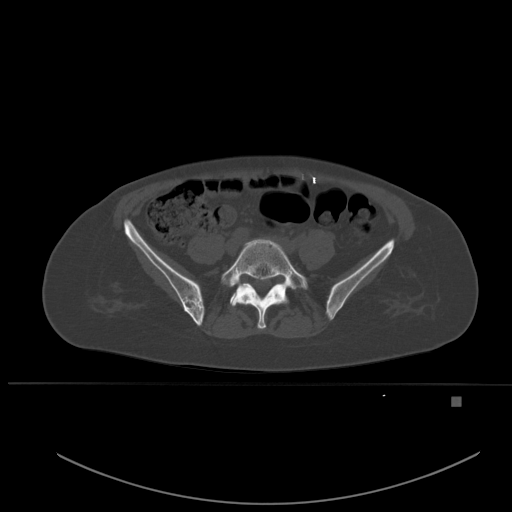
CT including the spine, one axial slice; position 153 of 651 along the scan axis; bone window (W 1800 / L 400 HU); 512 × 512 image matrix, field of view 443 × 443 mm. Female patient, age 49 years. From the clinical record (not read from this slice): primary cancer: breast.
Annotated regions visible in this slice (semi-automatically segmented with operator editing):
- L5 vertebra: bounding box <221,239,308,329> (left, top, right, bottom; pixels)